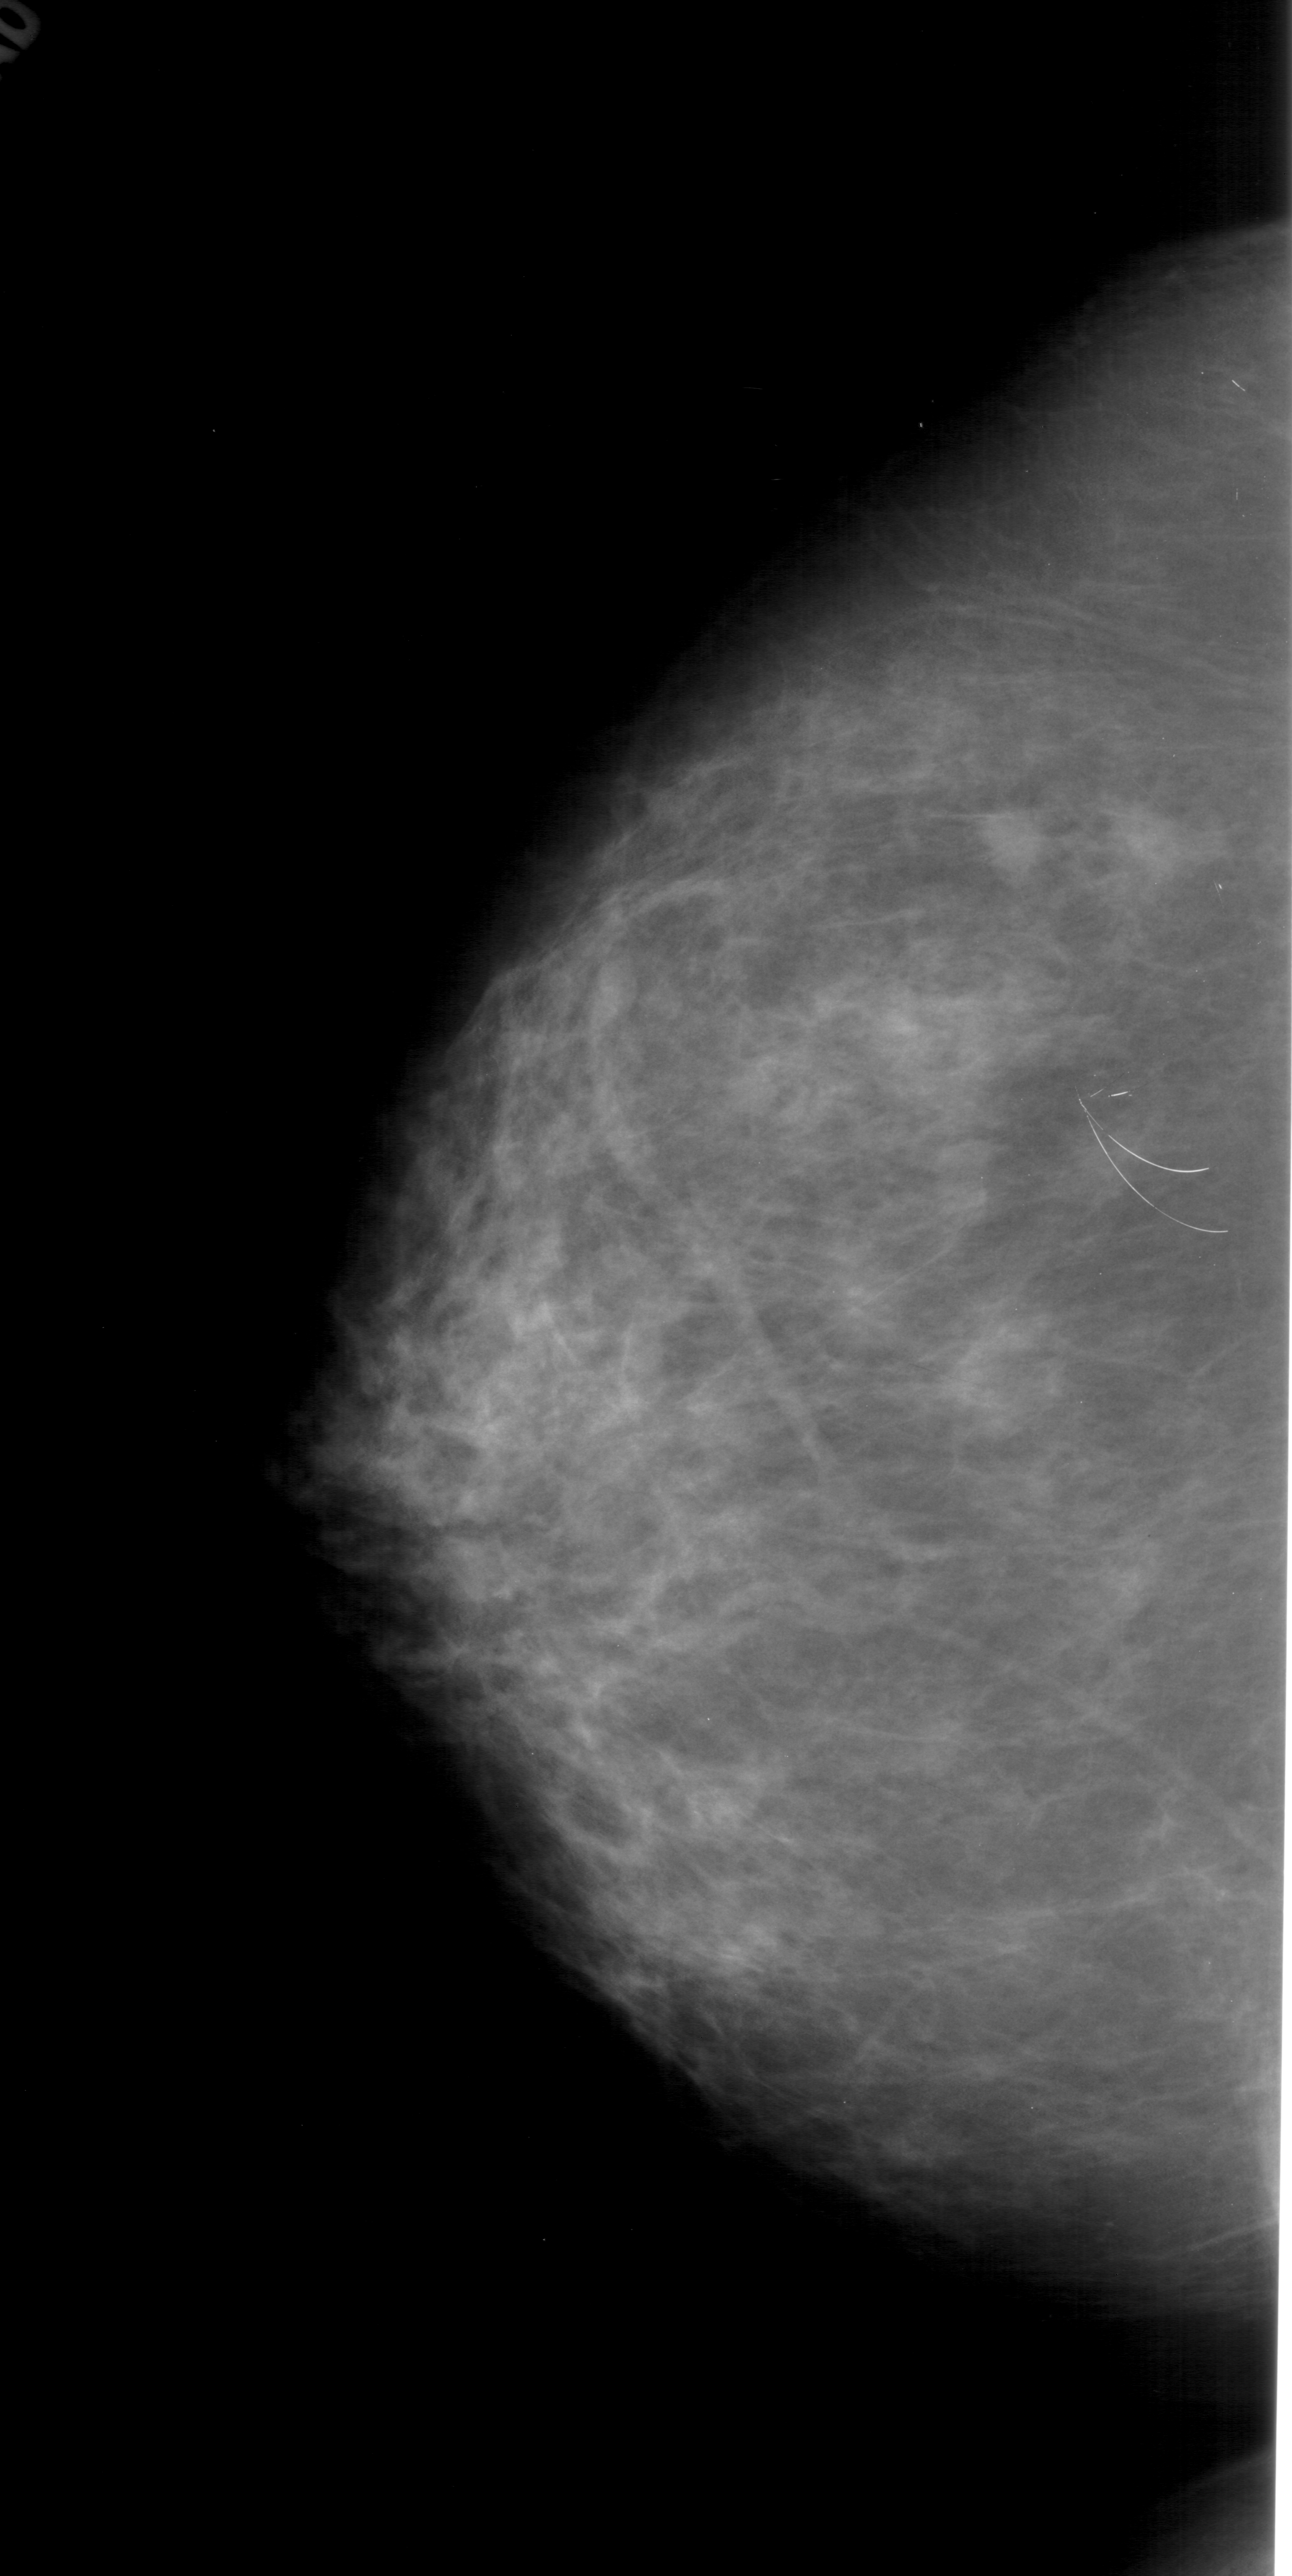
Digitized screen-film mammogram, left breast, craniocaudal (CC) view, breast composition: heterogeneously dense (BI-RADS density category 3 of 4).
Marked findings (only marked abnormalities are described; nothing is implied about the rest of the image): mass, shape irregular, margins ill defined; BI-RADS assessment category 4; pathology result (as recorded, not read from the image): malignant.